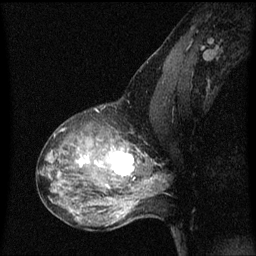
Breast MRI (dynamic contrast-enhanced), one sagittal slice; slice 38 of 60 in the series (ordered by position); dynamic contrast-enhanced series, image 2 of 3 at this slice position (ordered by acquisition); 1.5 T; TE 4.2 ms, TR 8 ms; 2 mm slice thickness; 256 × 256 image matrix. Patient: female, 50 years.
Structures marked on this image (semi-automatic segmentation, software-assisted and operator-edited):
- analysis volume of interest (the breast-tissue region the enhancement analysis was run in; not a lesion): bounding box [x1, y1, x2, y2] px = [91, 126, 141, 189]
- tumour enhancement mask (voxels above the 70 % enhancement threshold inside the analysis volume of interest): [95, 148, 135, 177]